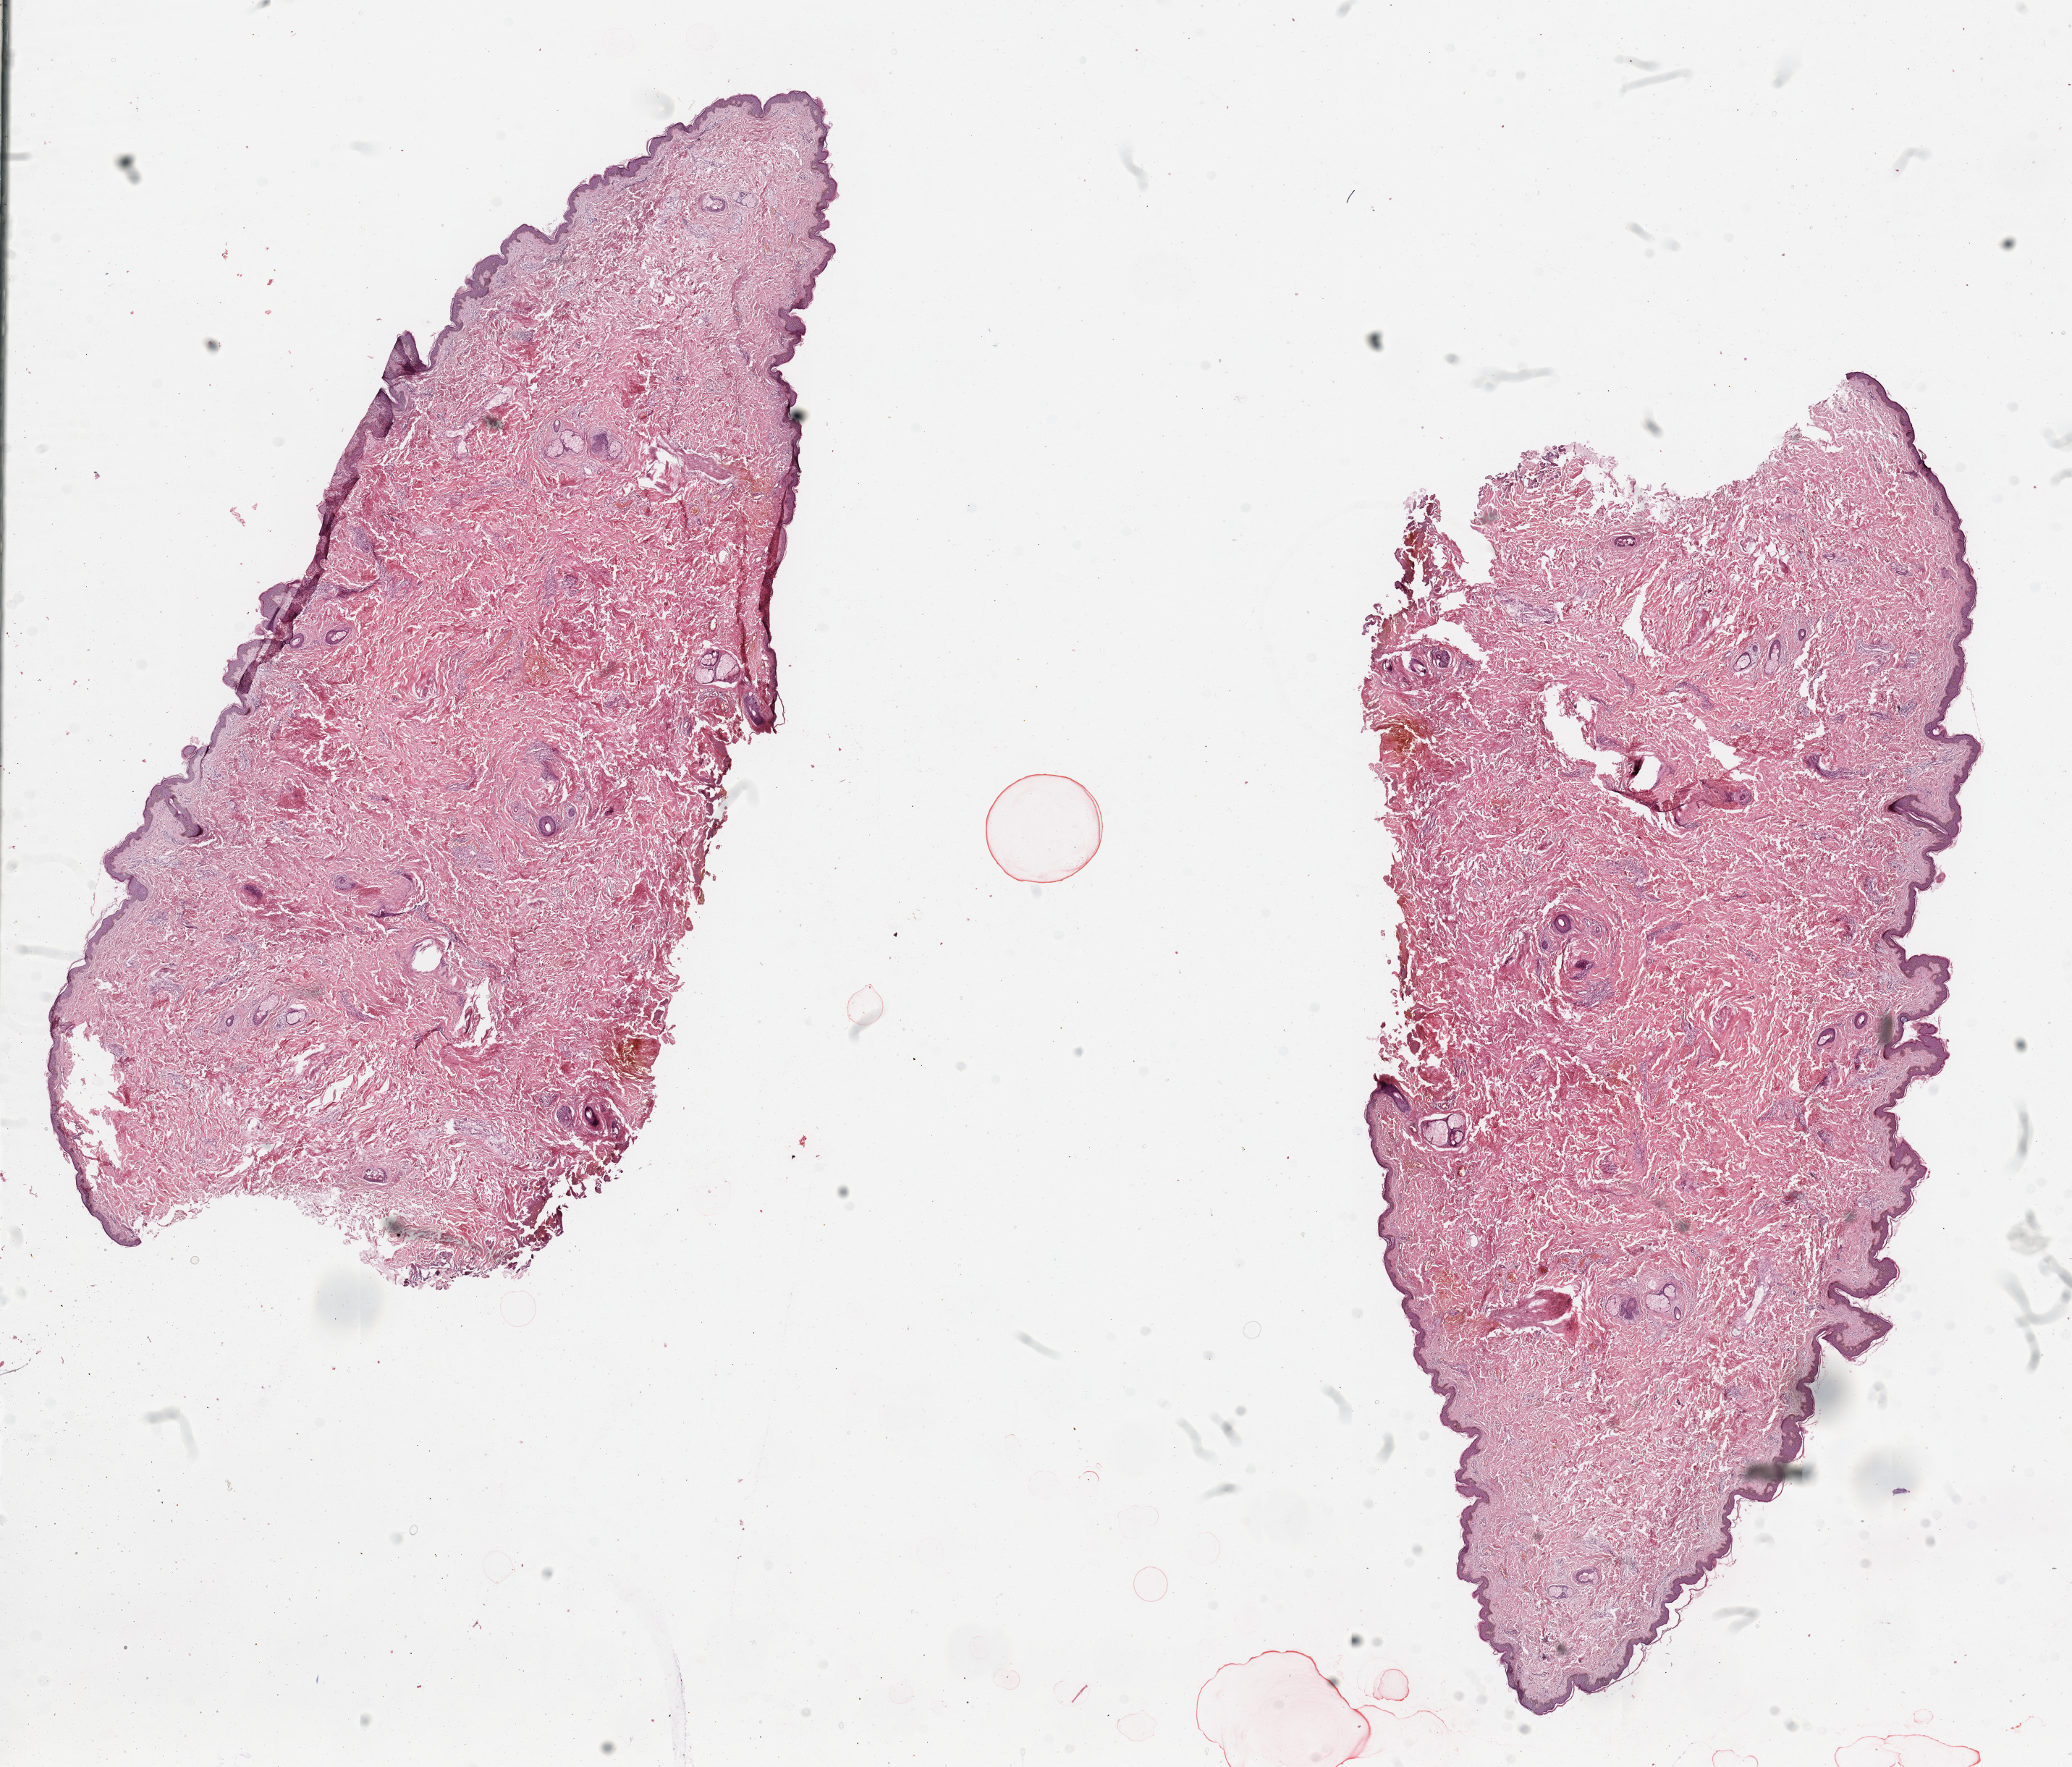
Hematoxylin and eosin (H&E) stained whole-slide image, shown as a low-resolution overview of the whole scanned area (about 22.6 x 19.3 mm, slide scanned at 20x), normal (non-tumour) tissue sample. 42-year-old male patient.
- this section: normal (non-tumour) tissue from the same patient
- patient diagnosis (cohort enrolment): sarcoma (site not recorded at cohort level)